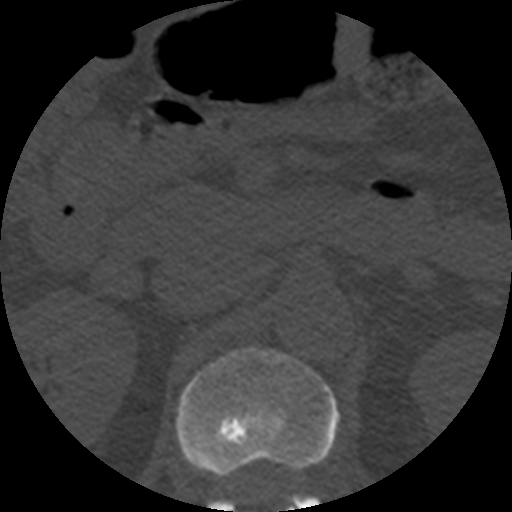
CT including the spine, one axial slice; position 196 of 508 along the scan axis; reconstruction kernel STANDARD; 120 kVp; bone window (W 1800 / L 400 HU); 1.25 mm slice thickness; 512 × 512 image matrix. Patient age 57 years. Case-level facts recorded for this patient, not image findings: primary cancer: prostate.
Outlined on this slice (semi-automatic segmentation, software-assisted and operator-edited):
- L1 vertebra: bounding box (x1, y1, x2, y2) in pixels: (177, 347, 339, 512)